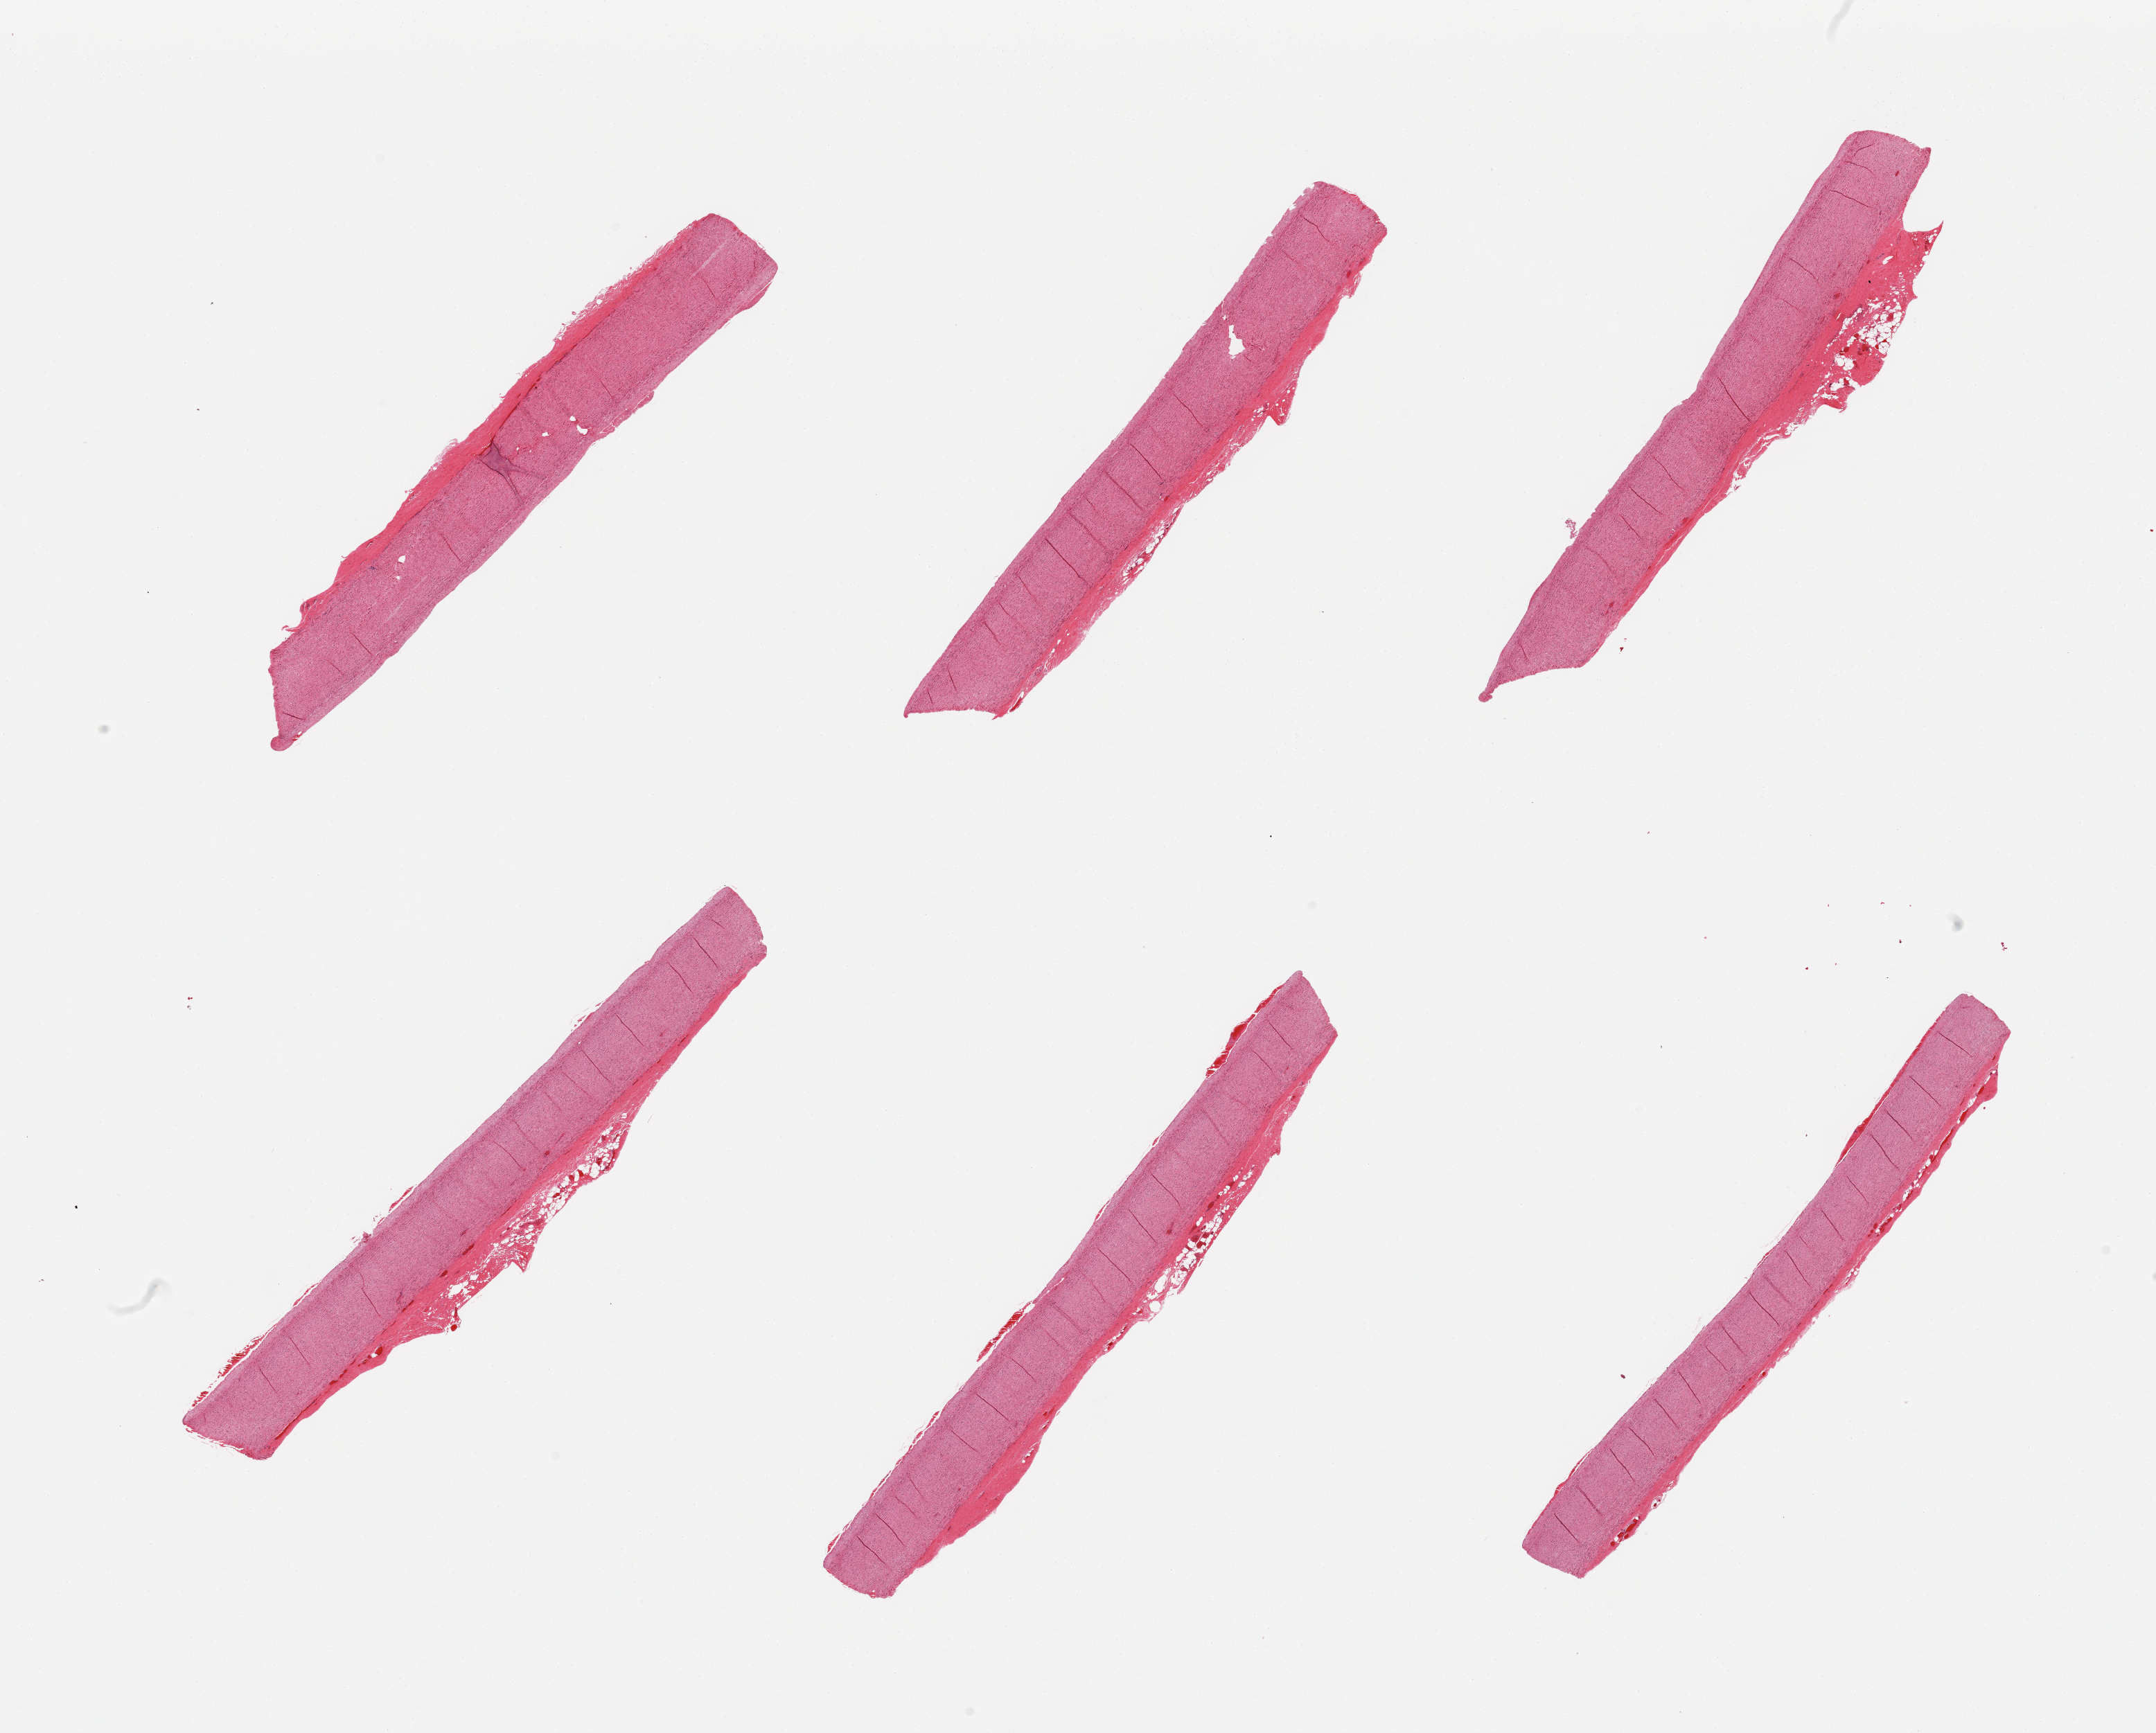
Whole-slide image, haematoxylin and eosin stain — a low-resolution overview of the entire scanned area, about 24.6 x 19.8 mm (from a 20x scan), PAXgene-fixed, paraffin-embedded tissue, section of aorta (target tissue), donor tissue sample. Donor sex: male.
Review note (as recorded): 6 pieces; well trimmed.